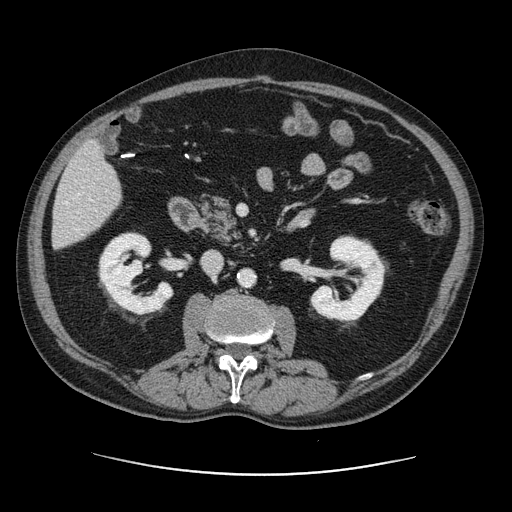
Contrast-enhanced abdominal CT, one axial slice. Position 44 of 141 along the scan axis. 120 kVp. Soft-tissue window (W 400 / L 40 HU). 2.5 mm slice thickness. 512 × 512 image matrix. Male patient, age 72 years. From the clinical record (not read from this slice): diagnosis: colorectal cancer liver metastases, imaged before liver resection; multiple liver metastases: yes.
Outlined on this slice (manually delineated by an expert):
- hepatic veins: bounding box [x1, y1, x2, y2] px = [65, 193, 92, 204]
- liver: [52, 143, 121, 248]
- planned liver remnant (the part of the liver to remain after resection): [52, 154, 121, 248]
- portal vein (with intrahepatic branches): [76, 229, 78, 231]